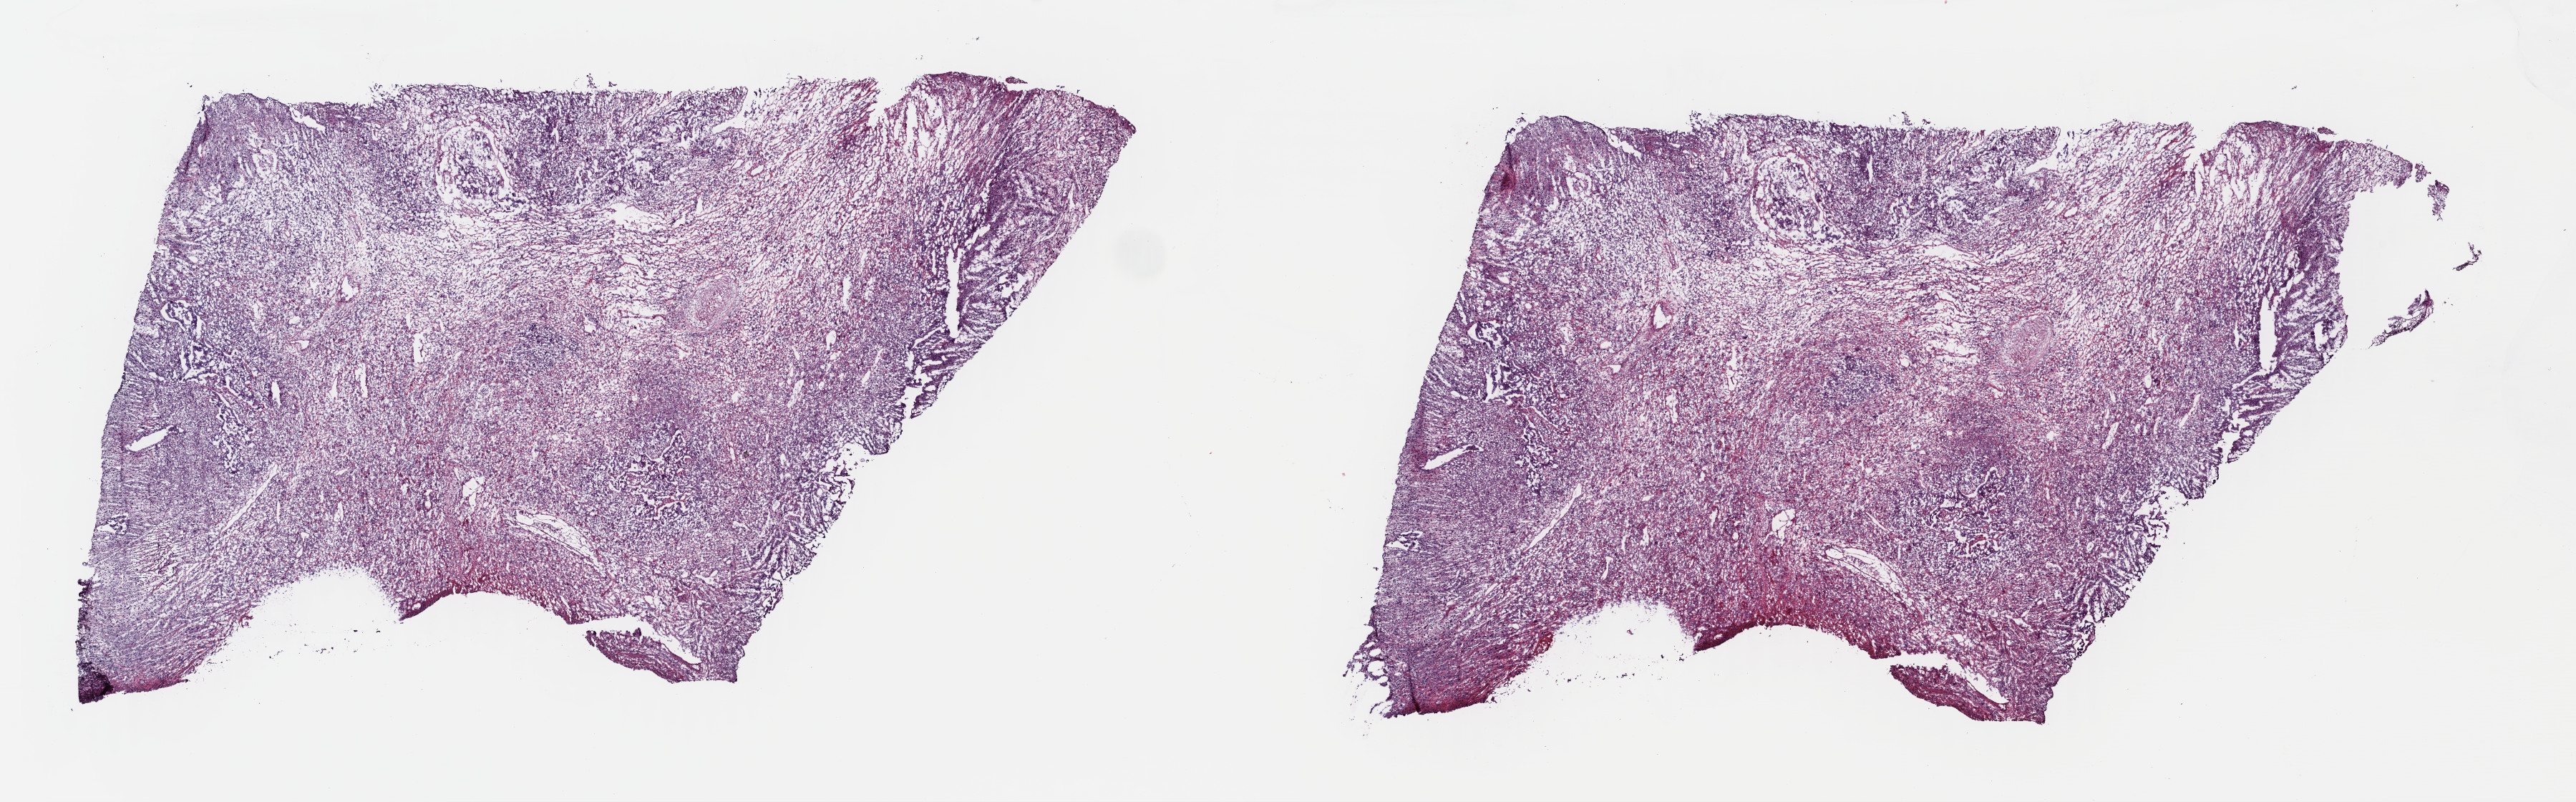
Whole-slide histology image, H&E-stained, low-resolution overview of the scanned area, about 28.3 x 8.8 mm (acquisition: 40x scan), frozen section, sample: primary tumour, uterus. Female, age 67 years at initial diagnosis. Slide review estimates, as recorded: tumour cells 90%, tumour nuclei 100%, normal cells 0%, stromal cells 10%, necrosis 0%. Infiltration values recorded for this section: lymphocyte infiltration 4%, monocyte infiltration 1%, neutrophil infiltration 0%.
* FIGO stage: IIIC
* pathologic diagnosis: Mullerian mixed tumor (endometrium)